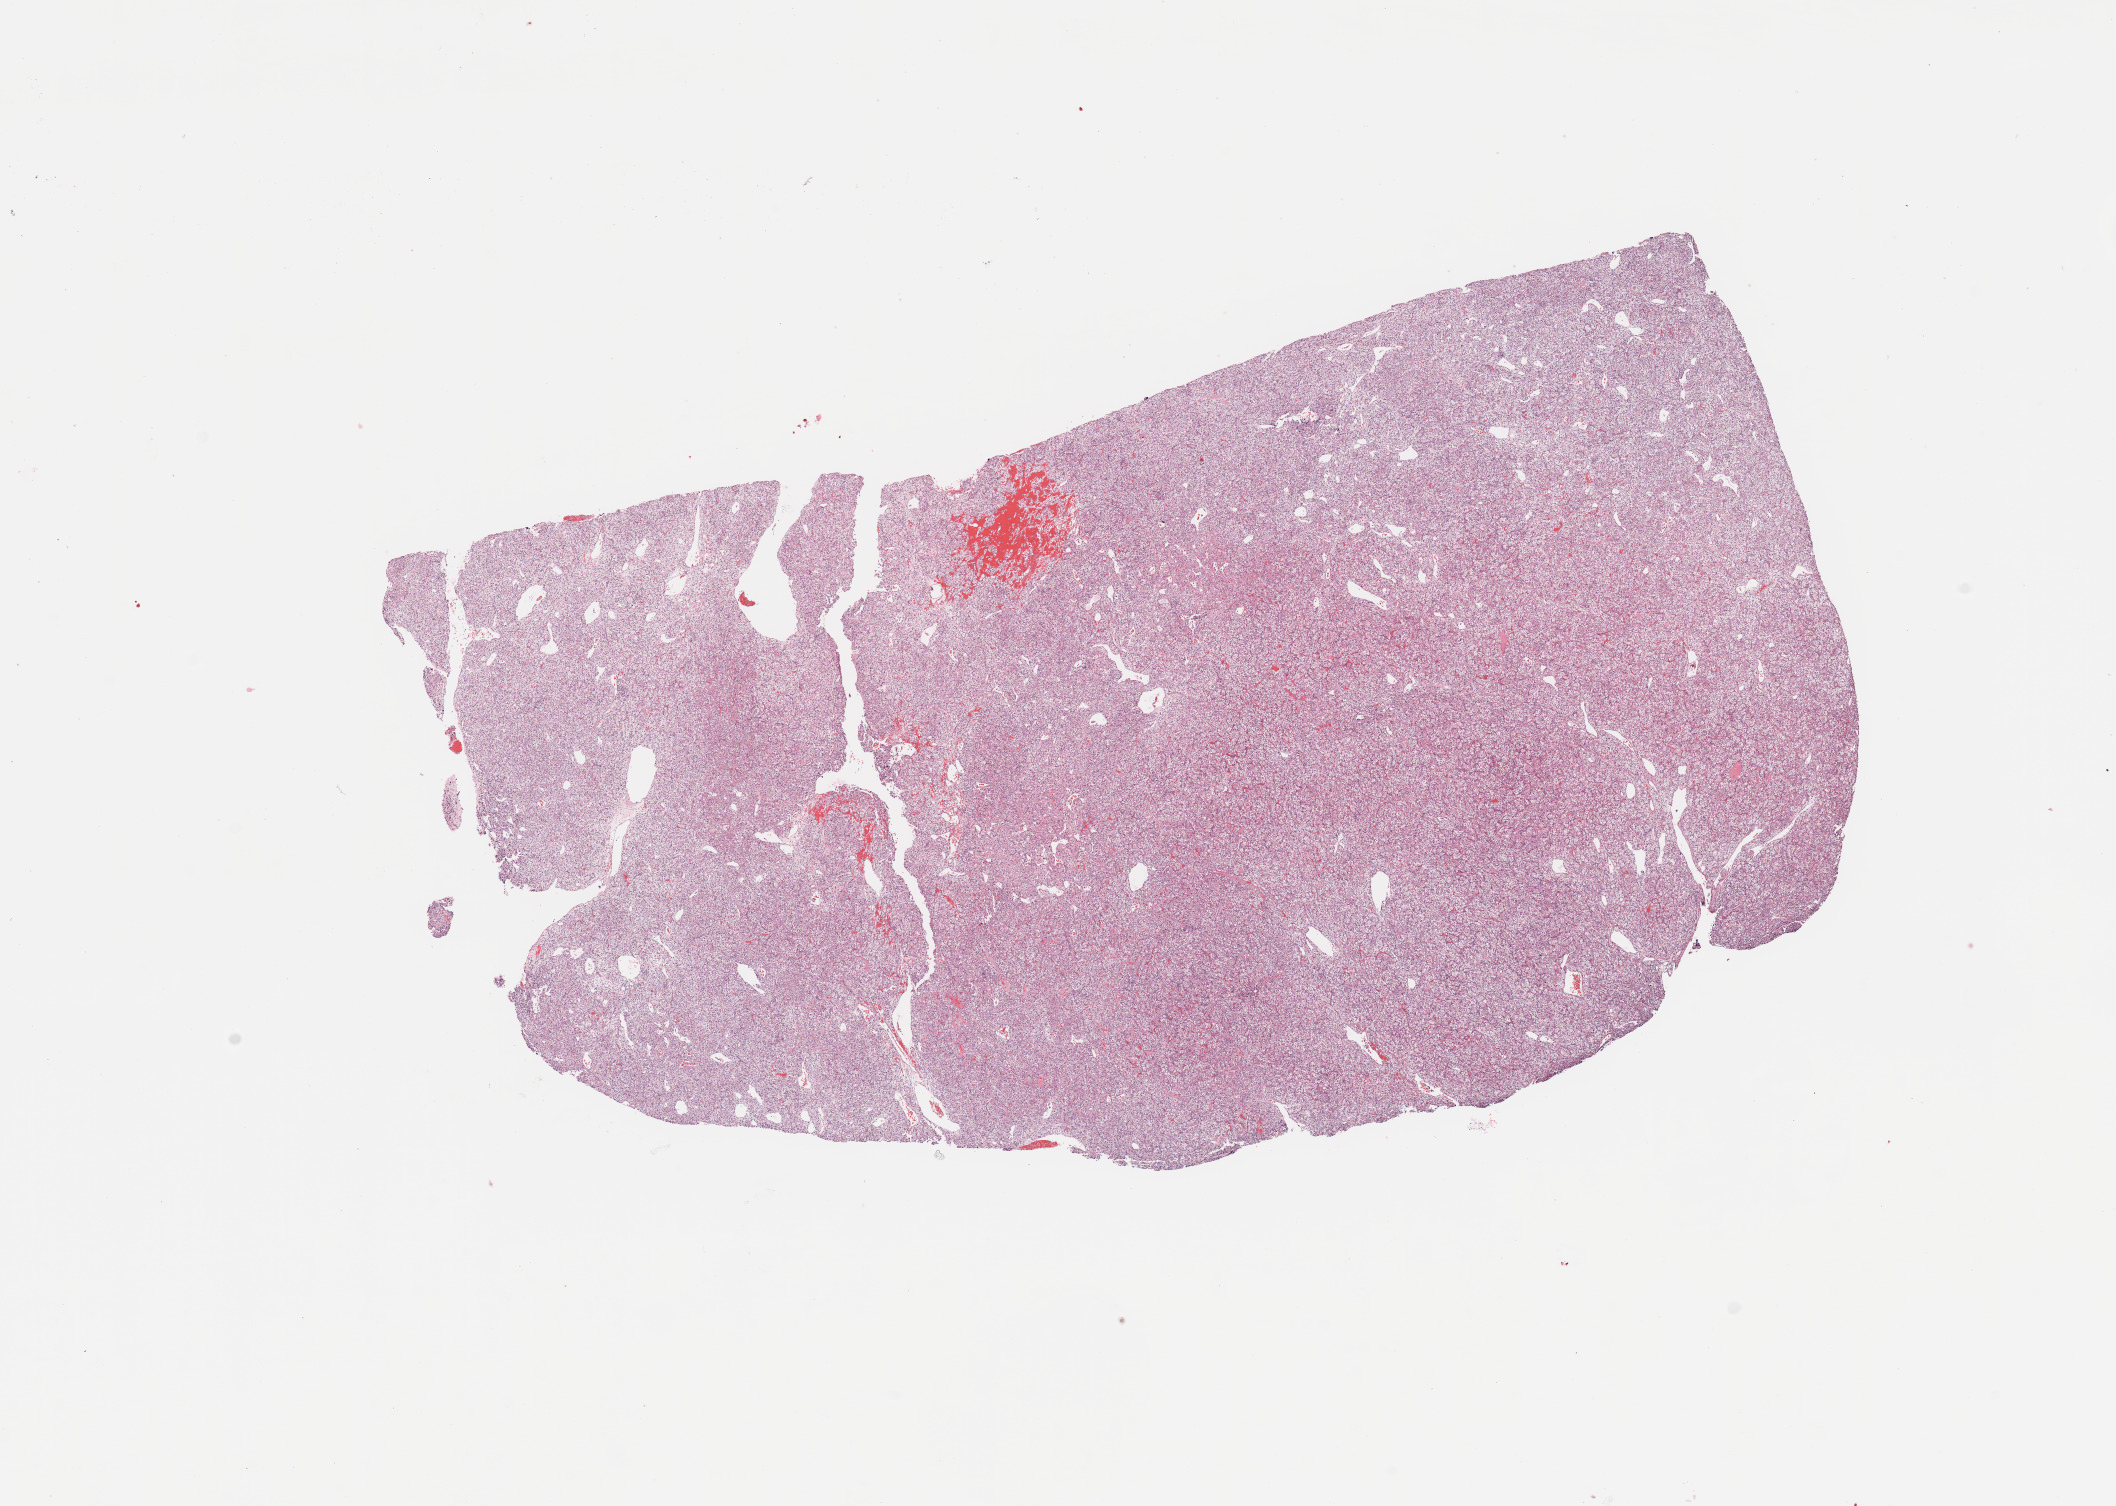
Digitized H&E-stained tissue section (whole slide) — shown as a low-resolution overview of the whole scanned area (about 16.7 x 11.9 mm). Tumour tissue sample, sampled site: kidney. Male, 76 y/o. Histologic grade: G3 (poorly differentiated). Pathologist review of this section (percent, as recorded): tumour nuclei 95%, necrosis 0%.
Primary tumour site (as recorded): lower pole. Diagnosis: Renal cell carcinoma, NOS. AJCC pathologic stage: III.